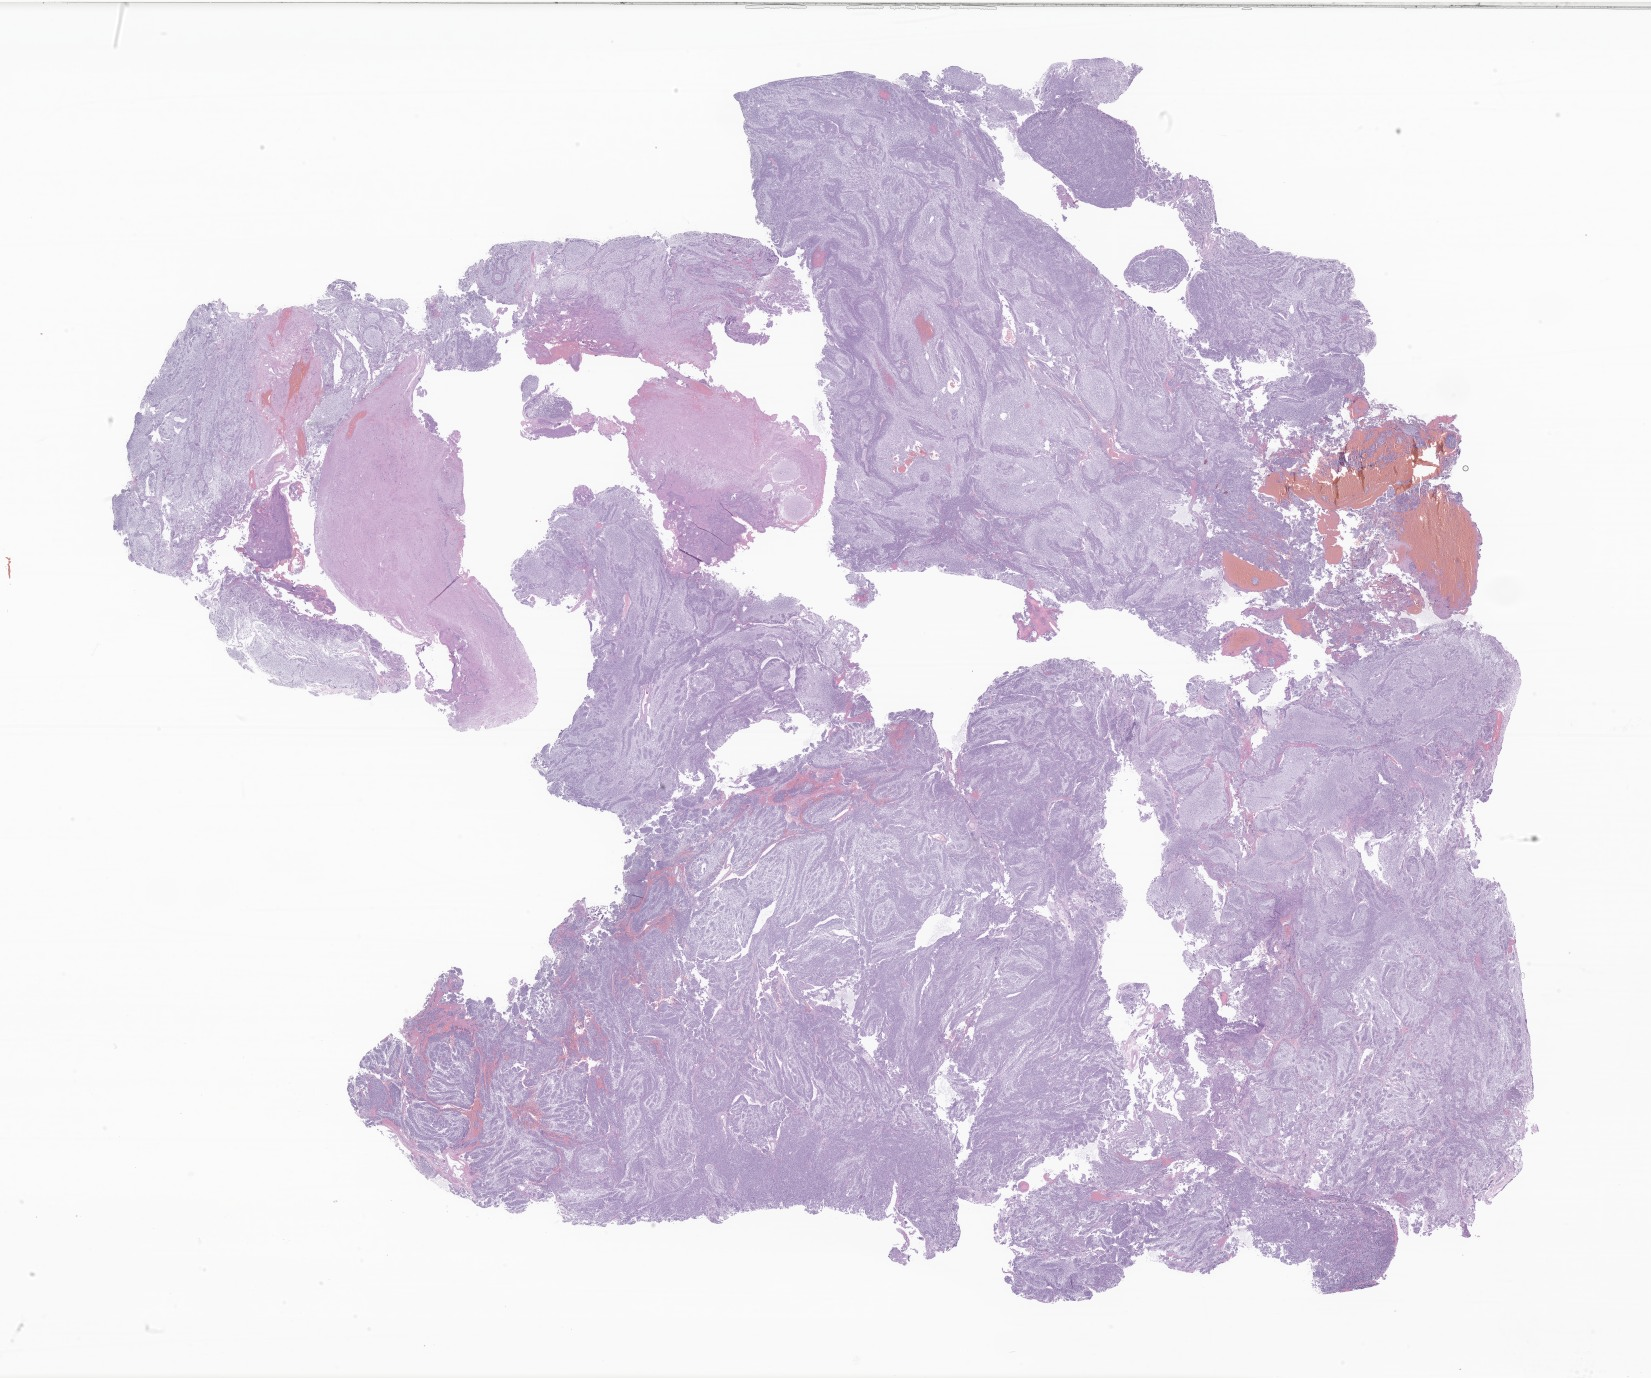
H&E whole-slide image of tumor tissue from the brain, whole scanned area (about 27.8 x 23.2 mm) shown as a low-resolution overview; FFPE section. Patient: female, age 684 days.
* recorded diagnosis: Medulloblastoma, NOS